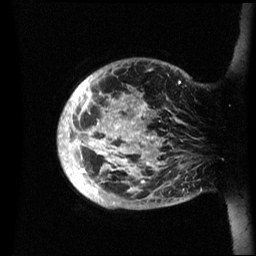
Breast MRI (dynamic contrast-enhanced), one sagittal slice; position 8 of 60 along the scan axis; dynamic contrast-enhanced series, image 2 of 3 at this slice position (ordered by acquisition); 1.5 T; TE 4.2 ms, TR 8.4 ms; 256 × 256 image matrix, field of view 230 × 230 mm. Female patient, age 48 years.
Structures marked on this image (semi-automatic segmentation, software-assisted and operator-edited):
- analysis volume of interest (the breast-tissue region the enhancement analysis was run in; not a lesion): bounding box <57,58,201,210> (left, top, right, bottom; pixels)
- tumour enhancement mask (voxels above the 70 % enhancement threshold inside the analysis volume of interest): <57,81,181,193>